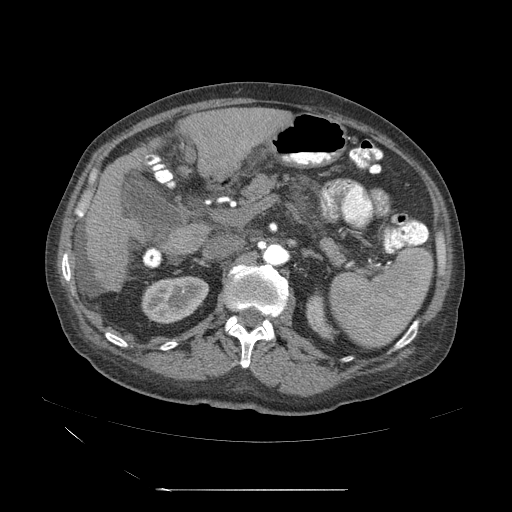
Contrast-enhanced abdominal CT (liver protocol), one axial slice; position 20 of 71 along the scan axis; 120 kVp; soft-tissue window (W 400 / L 40 HU); 2.5 mm slice thickness; 512 × 512 image matrix. Case-level facts recorded for this patient, not image findings: diagnosis: hepatocellular carcinoma (patient treated with transarterial chemoembolisation; whether this scan precedes or follows treatment is not stated here); TNM stage (as recorded): Stage-II; Child-Pugh class: A; tumour size: 1 cm.
Outlined on this slice (semi-automatically segmented with operator editing):
- abdominal aorta: bounding box [x1, y1, x2, y2] px = [263, 244, 286, 269]
- liver parenchyma outside the tumour (the mass and vessels are separate outlines, so this box may not span the whole liver): [84, 183, 130, 292]
- liver vessels: [201, 209, 246, 261]